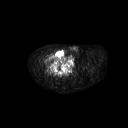
FDG PET of an extremity soft-tissue mass (from a PET/CT study), one axial slice; slice 273 of 311 in the series (ordered by position); 128 × 128 image matrix. Patient: male, 50 years. From the clinical record (not read from this slice): histological type: undifferentiated - pleiomorphic; grade: high; site of the primary tumour: right thigh.
Annotated regions visible in this slice (expert contour drawn on MRI and transferred to this co-registered scan by the dataset authors):
- gross tumour volume including surrounding oedema: bounding box (x1, y1, x2, y2) in pixels: (46, 49, 66, 68)
- gross tumour volume (mass): (46, 49, 66, 68)